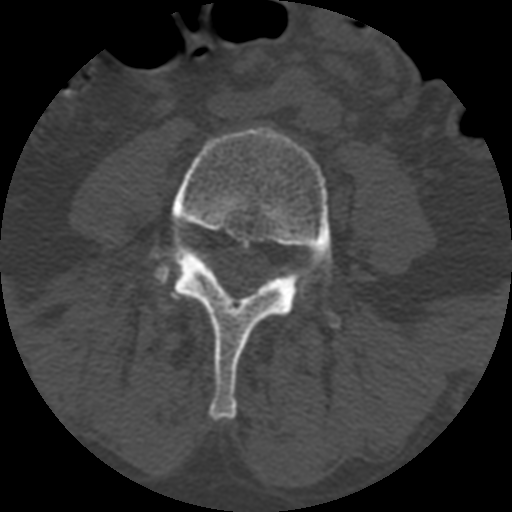
CT including the spine, one axial slice. Slice 279 of 399 in the series (ordered by position). Bone window (W 1800 / L 400 HU). 1.25 mm slice thickness. 512 × 512 image matrix, field of view 160 × 160 mm. Patient age 71 years. Case-level facts recorded for this patient, not image findings: primary cancer: prostate.
Annotated regions visible in this slice (semi-automatic segmentation, software-assisted and operator-edited):
- L4 vertebra: bounding box [x1, y1, x2, y2] px = [149, 128, 333, 421]
- L5 vertebra: [156, 262, 170, 284]